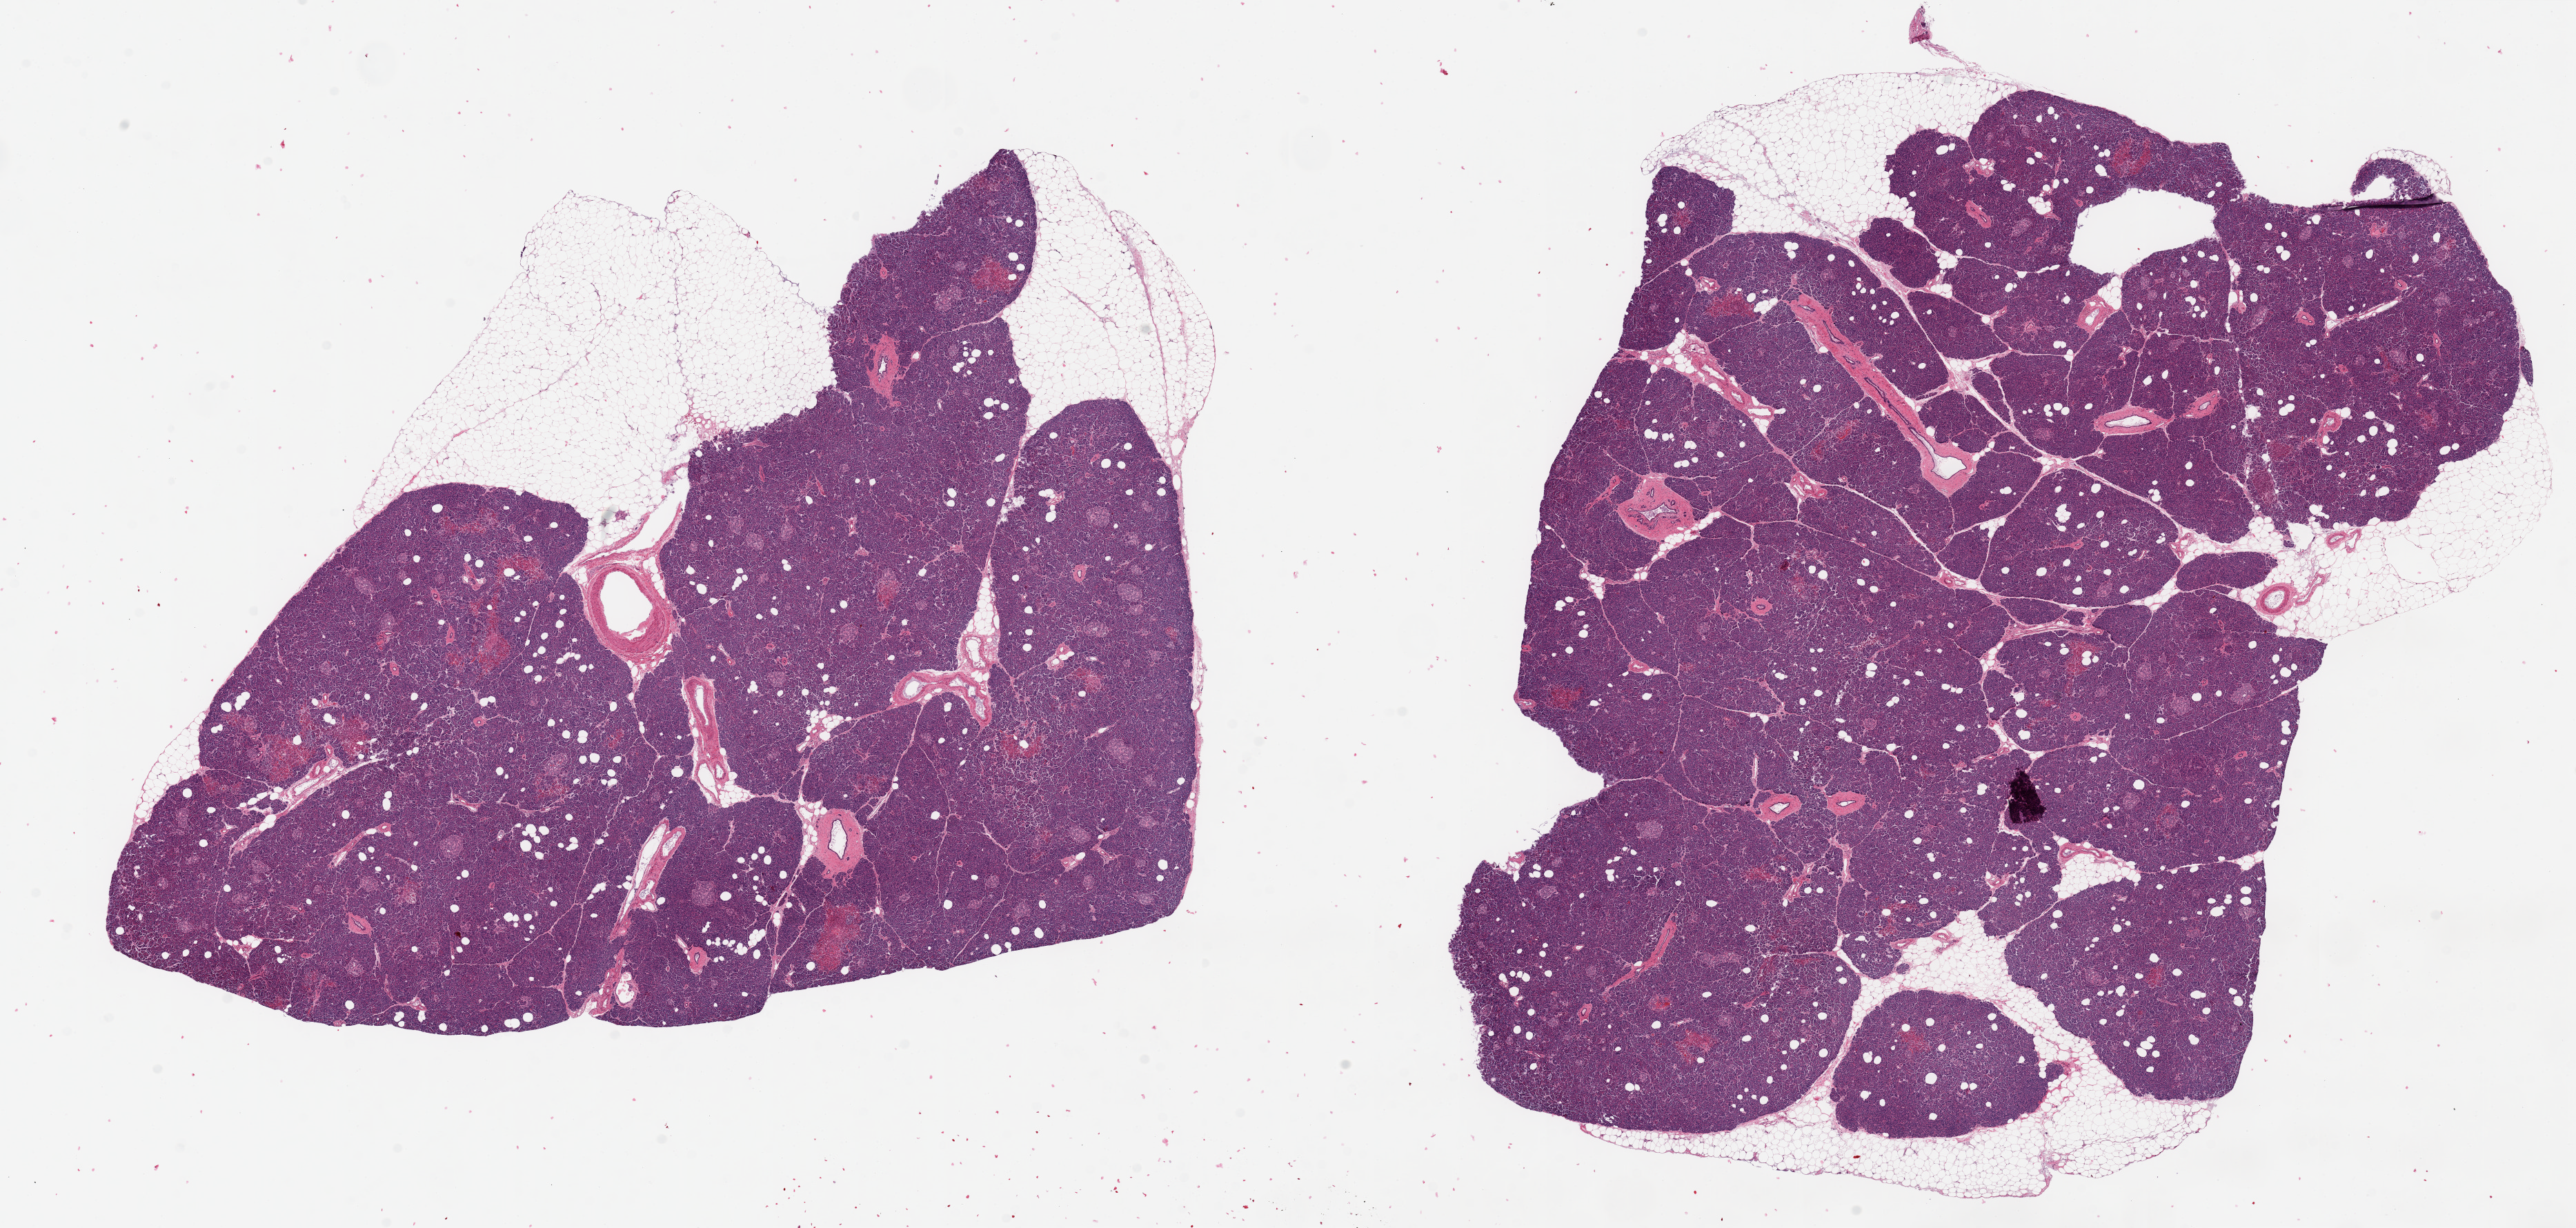
Digitized H&E-stained section, a low-resolution overview of the entire scanned area, about 29.5 x 14.1 mm (slide scanned at 20x), PAXgene-fixed, paraffin-embedded tissue, sampled site (target tissue): pancreas, donor tissue sample. Donor sex: male.
Reviewer comment on this tissue sample: 2 pieces, 12.5x10 & 14x13mm; Scattered eosinophilic foci in exocrine and endocrine tissue, some having infarcted centers and fibrin thrombi in capillaries.